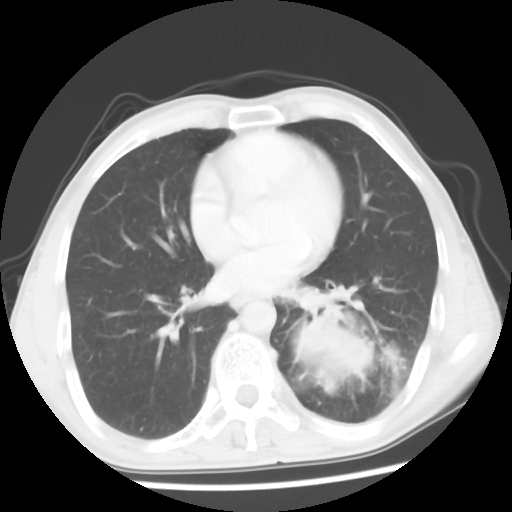
Chest CT, one axial slice; slice 25 of 56 in the series (ordered by position); reconstruction kernel STANDARD; lung window (W 1500 / L -600 HU); 512 × 512 image matrix. Male patient, age 60 years. From the clinical record (not read from this slice): clinical TNM (as recorded): T4 N0 M0.
Structures marked on this image (bounding box drawn by a radiologist):
- lung tumour (recorded histology: squamous cell carcinoma): bounding box <287,299,381,404> (left, top, right, bottom; pixels)